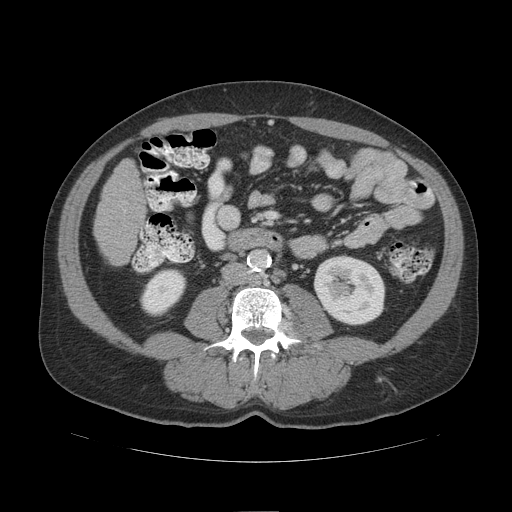
Contrast-enhanced abdominal CT (liver protocol), one axial slice; soft-tissue window (W 400 / L 40 HU); 512 × 512 image matrix, field of view 420 × 420 mm. From the clinical record (not read from this slice): diagnosis: hepatocellular carcinoma (patient treated with transarterial chemoembolisation; whether this scan precedes or follows treatment is not stated here); TNM stage (as recorded): Stage-IIIB; Child-Pugh class: A; tumour differentiation: poorly differentiated; tumour nodularity: multinodular.
Annotated regions visible in this slice (semi-automatically segmented with operator editing):
- liver parenchyma outside the tumour (the mass and vessels are separate outlines, so this box may not span the whole liver): box from (x=94, y=158) to (x=146, y=264) px